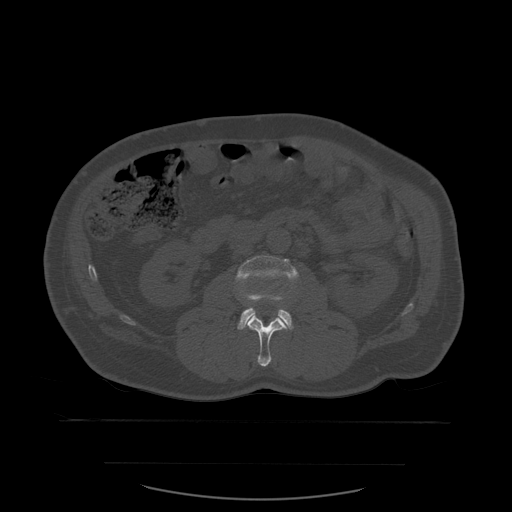
CT including the spine, one axial slice. Slice 206 of 590 in the series (ordered by position). Bone window (W 1800 / L 400 HU). 1.25 mm slice thickness. 512 × 512 image matrix, field of view 479 × 479 mm. Patient age 71 years. From the clinical record (not read from this slice): primary cancer: lung; vertebrae with lytic lesions (as recorded): T1, T2, L5, S1.
Annotated regions visible in this slice (semi-automatic segmentation, software-assisted and operator-edited):
- L2 vertebra: bounding box [x1, y1, x2, y2] px = [245, 298, 289, 367]
- L3 vertebra: [236, 256, 299, 330]